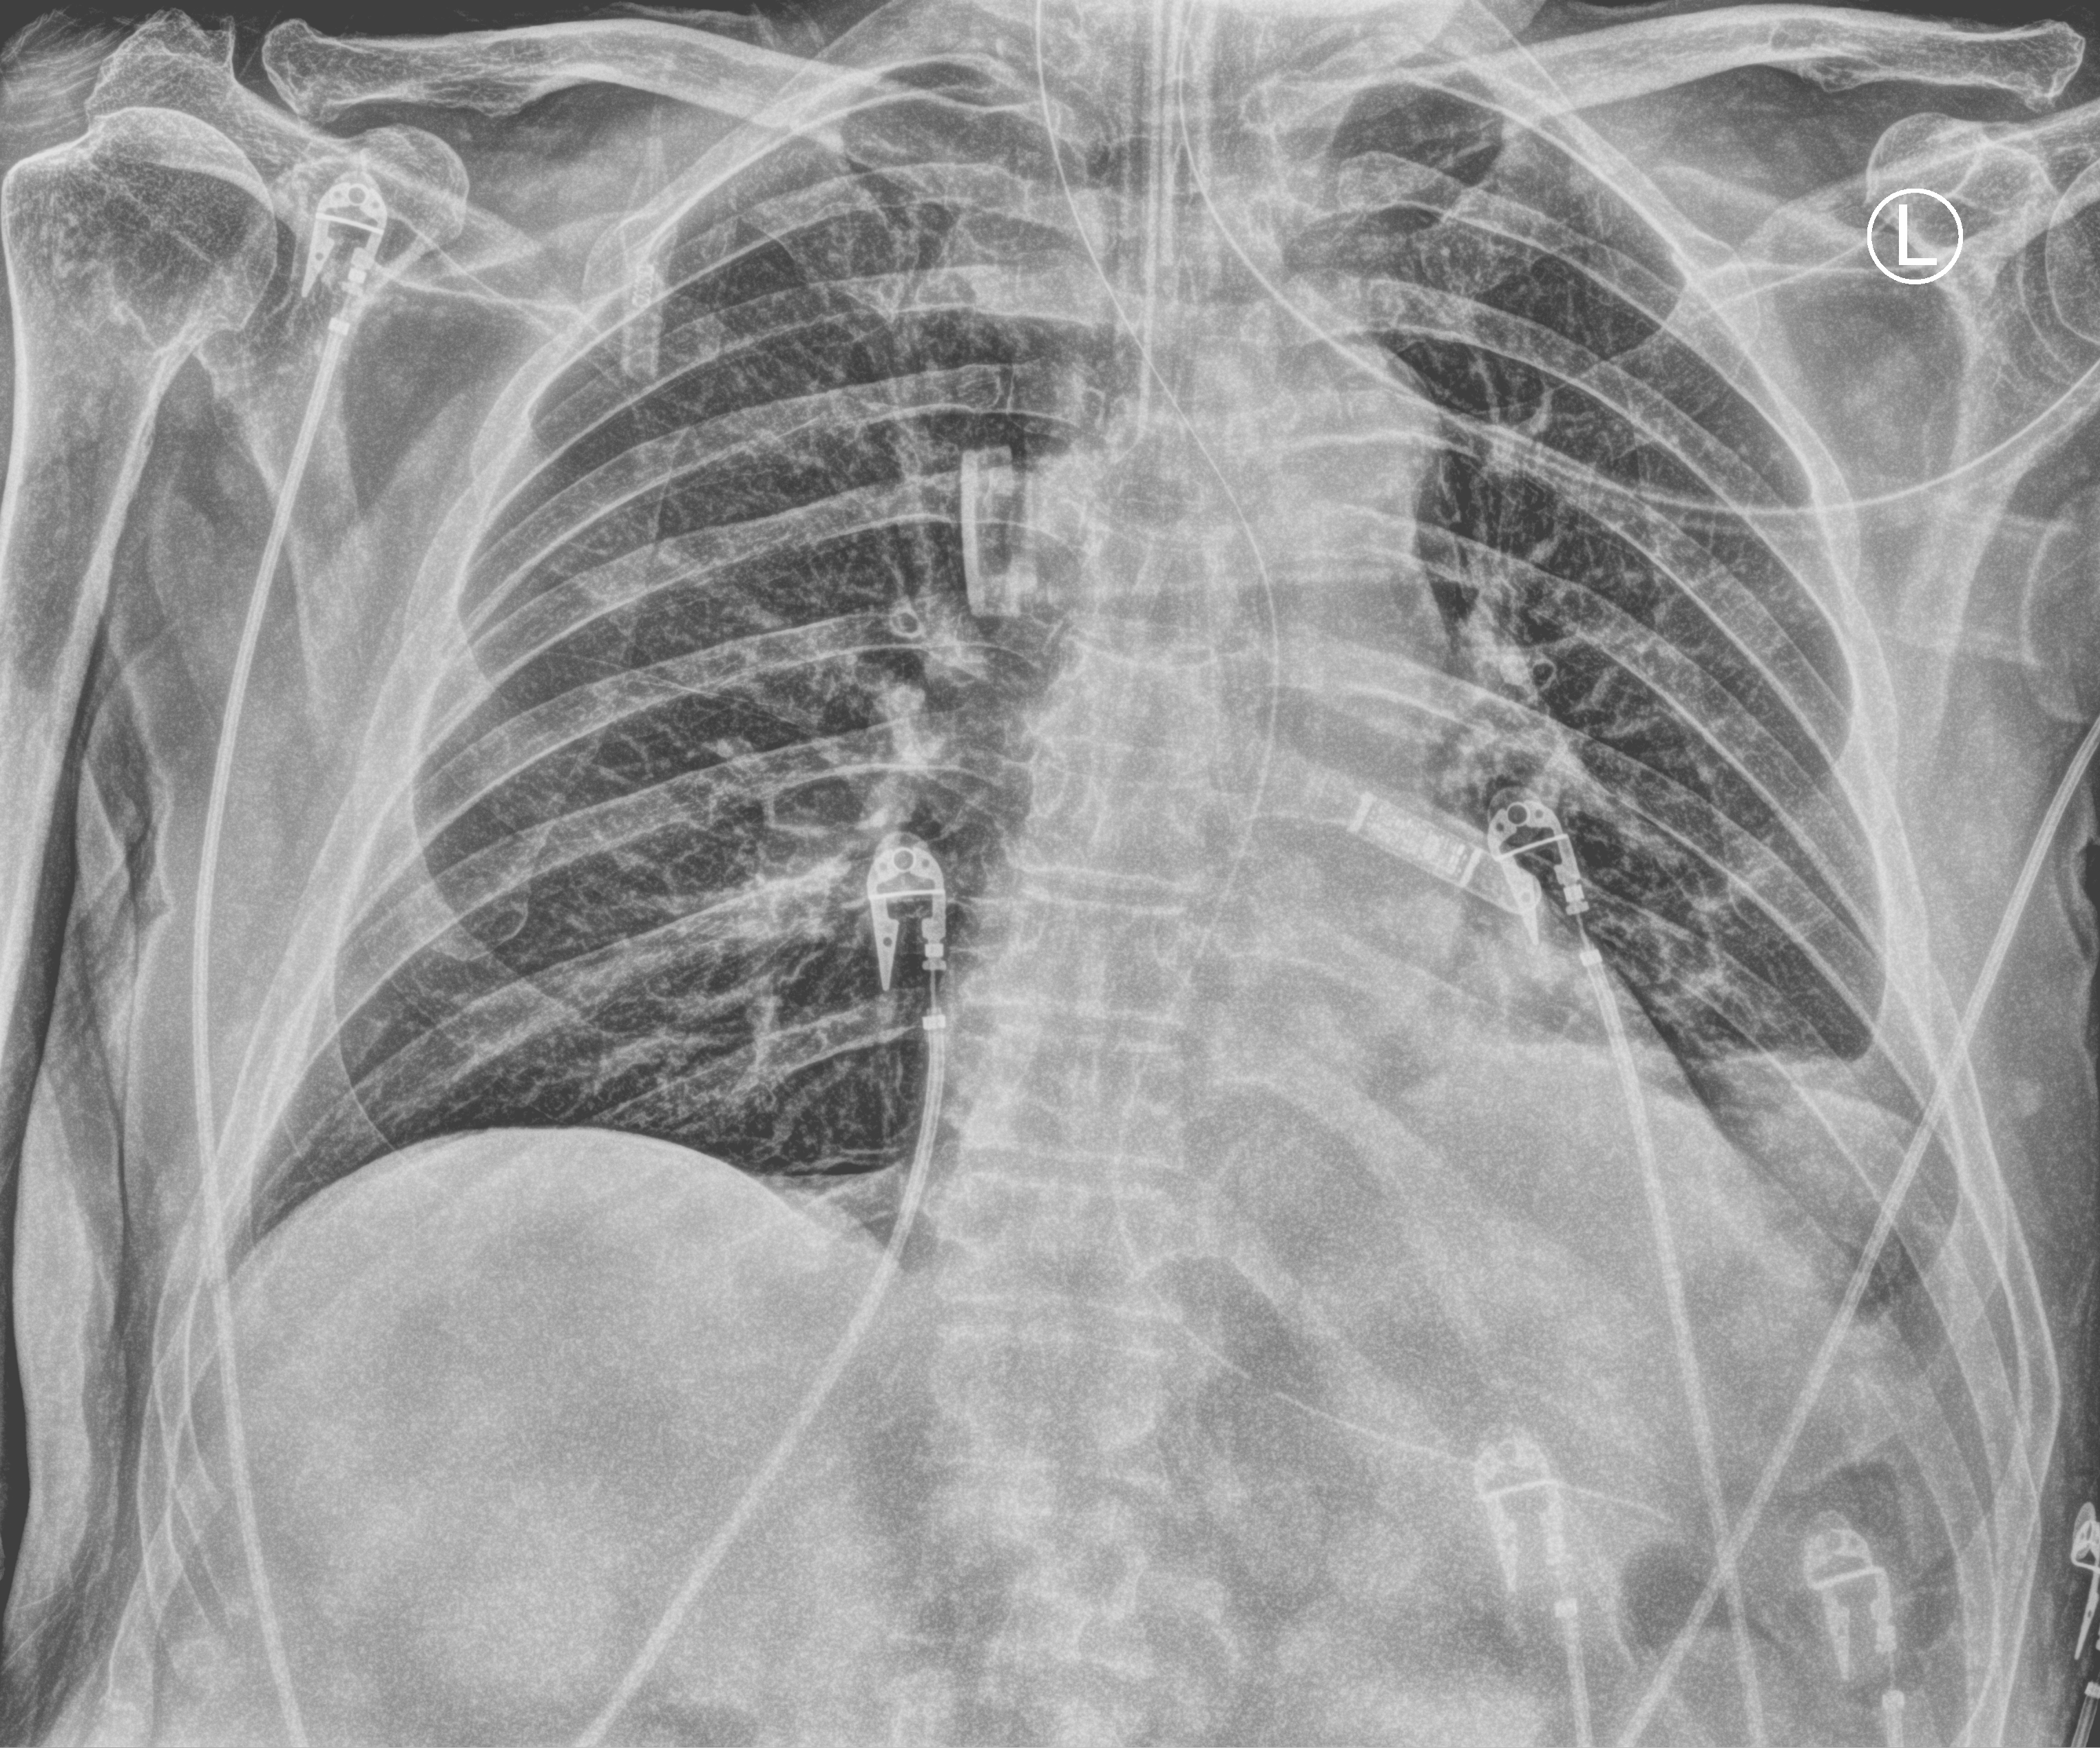
Bedside chest radiograph (computed radiography); anteroposterior (AP) projection. Male patient hospitalised with COVID-19, age 75–90 years.
Admission-level facts for this patient (not findings on this image; timing relative to this image not recorded): mechanically ventilated during this hospital stay: no; length of hospital stay: 1 day.